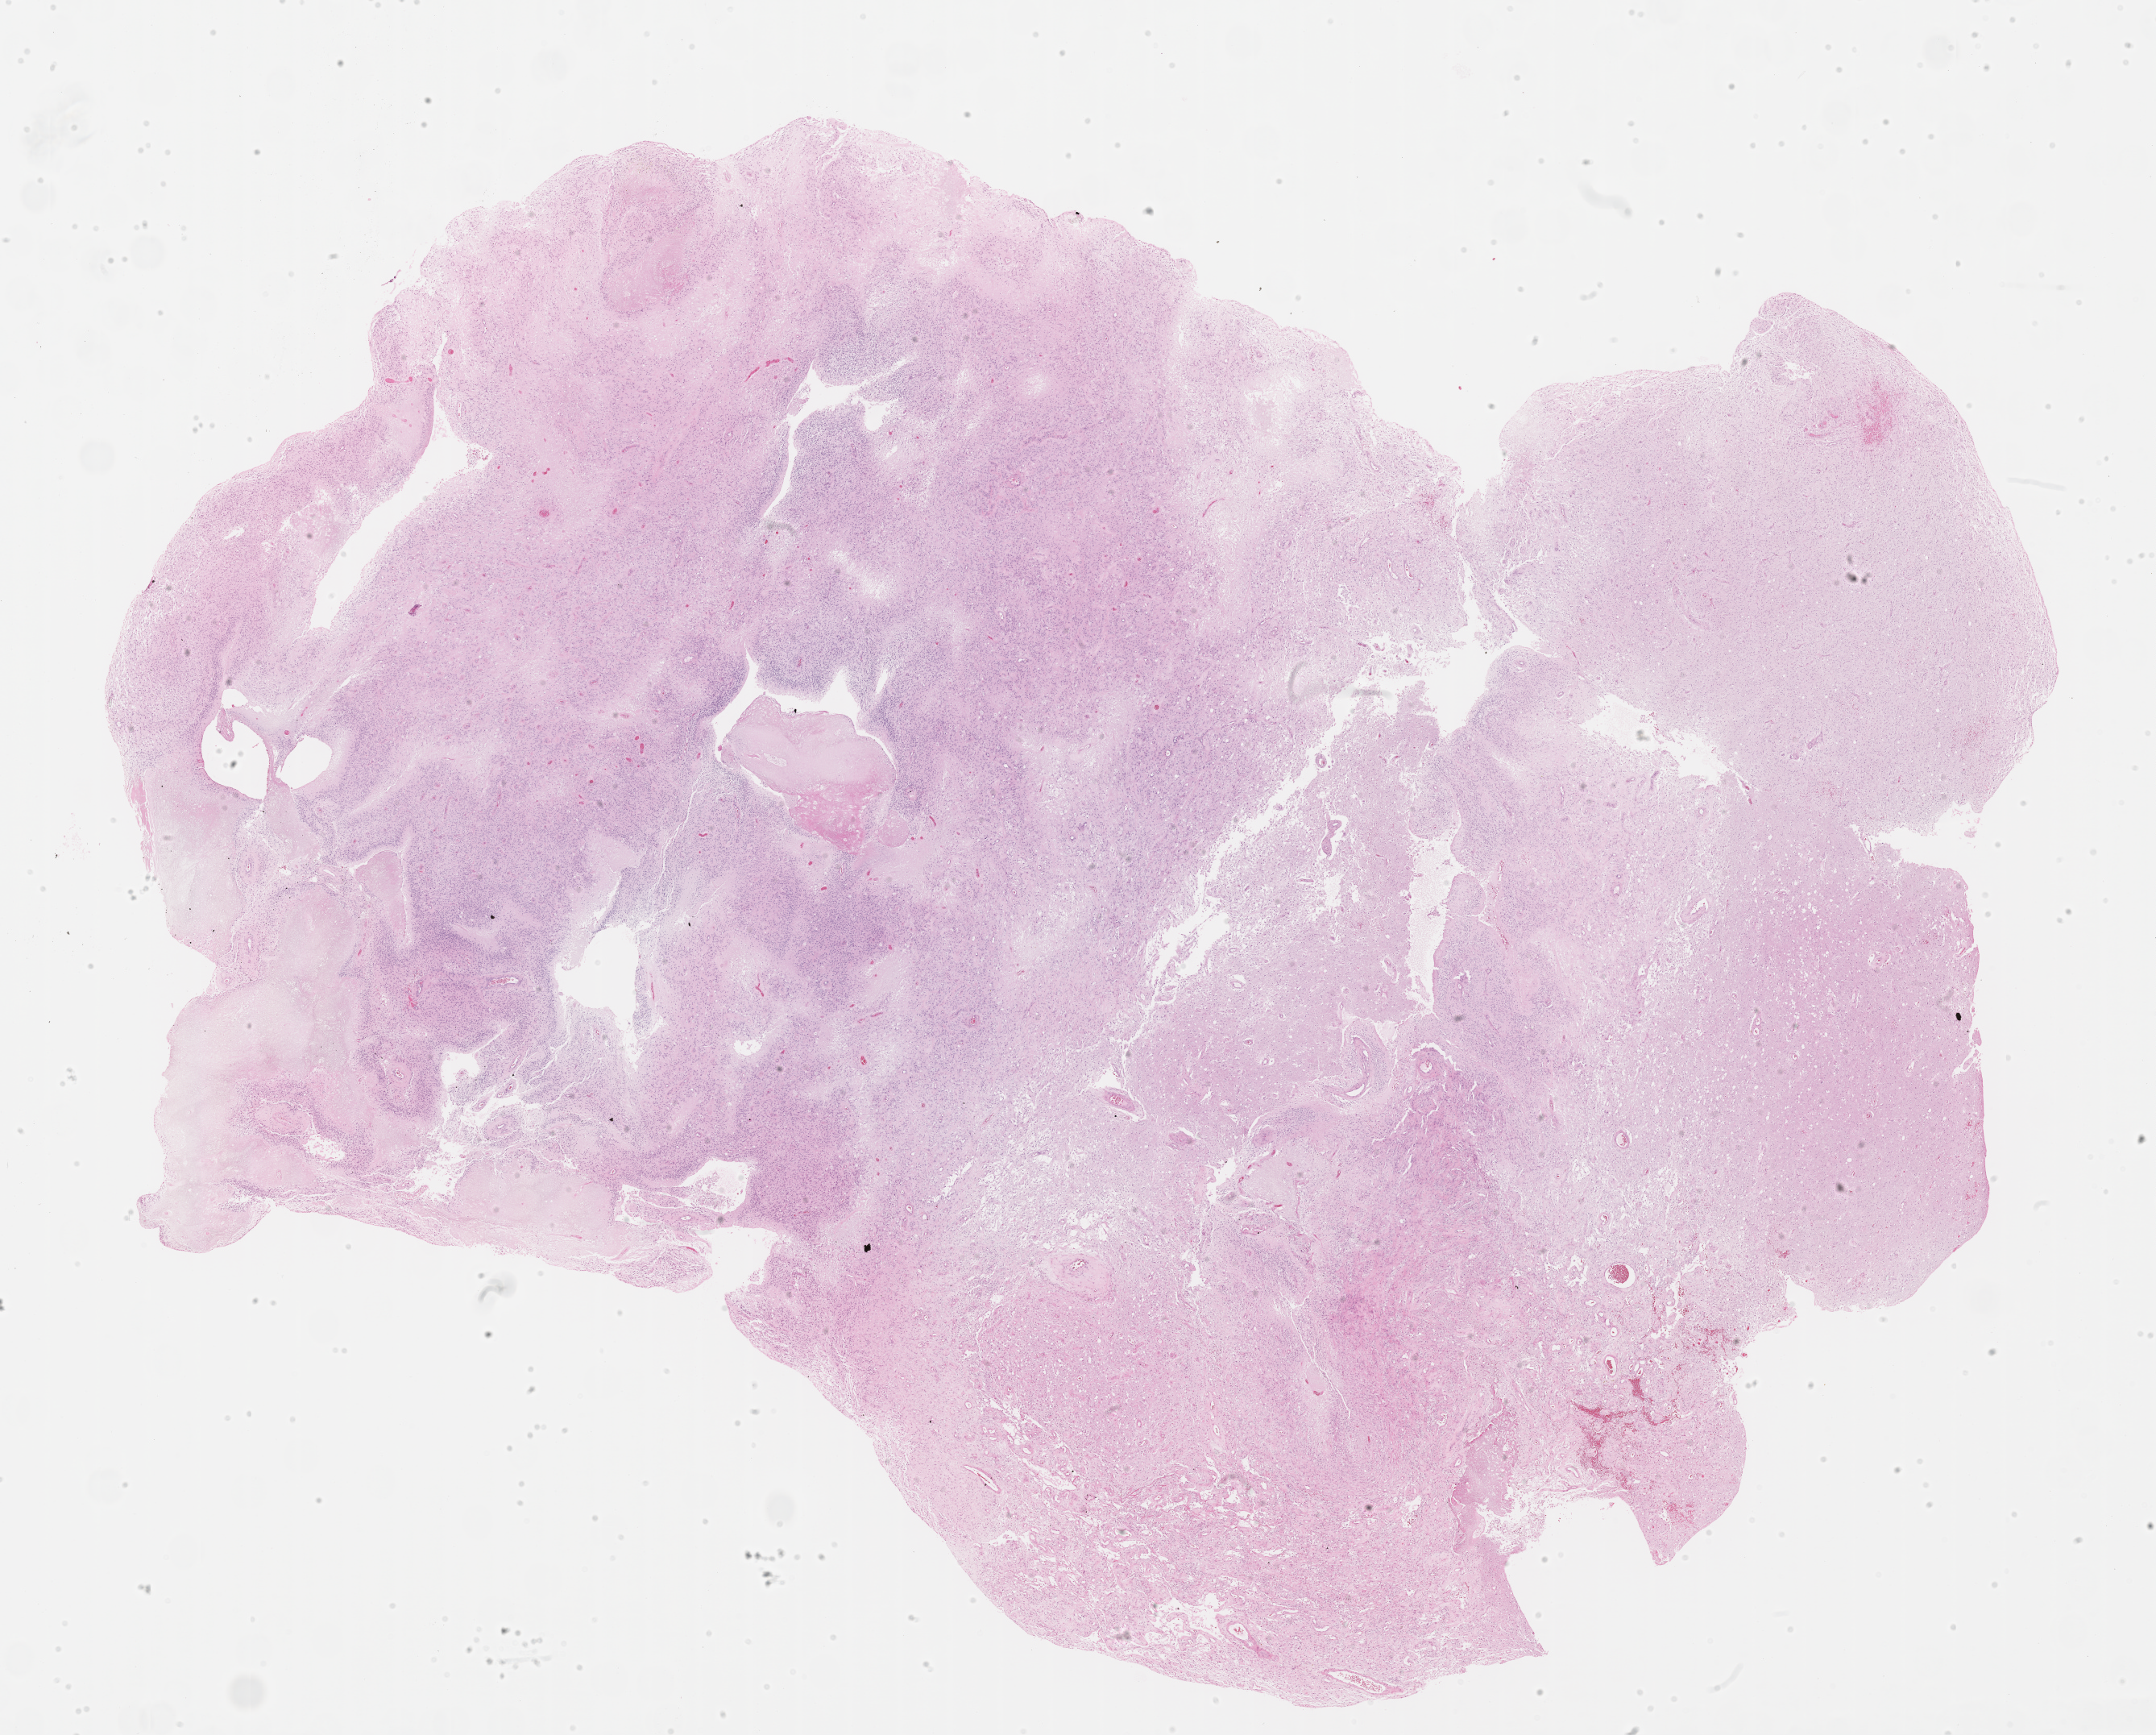
Whole-slide histology image, H&E-stained — a low-resolution overview of the entire scanned area, about 21.7 x 17.5 mm (from a 40x scan); formalin-fixed paraffin-embedded (FFPE) diagnostic section; brain, primary tumour sample. Patient: male, age at initial diagnosis 52 years.
* histologic diagnosis: Glioblastoma